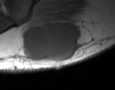
MRI of an extremity soft-tissue mass, one axial slice. Slice 18 of 35 in the series (ordered by position). MR volume resampled by the dataset authors to the PET/CT grid (not the native acquisition matrix). 115 × 90 image matrix. Male patient. From the clinical record (not read from this slice): histological type: pleiomorphic leiomyosarcoma; grade: high; site of the primary tumour: left buttock.
Outlined on this slice (expert contour drawn on MRI and transferred to this co-registered scan by the dataset authors):
- gross tumour volume including surrounding oedema: bounding box (x1, y1, x2, y2) in pixels: (24, 21, 82, 60)
- gross tumour volume (mass): (24, 21, 81, 60)